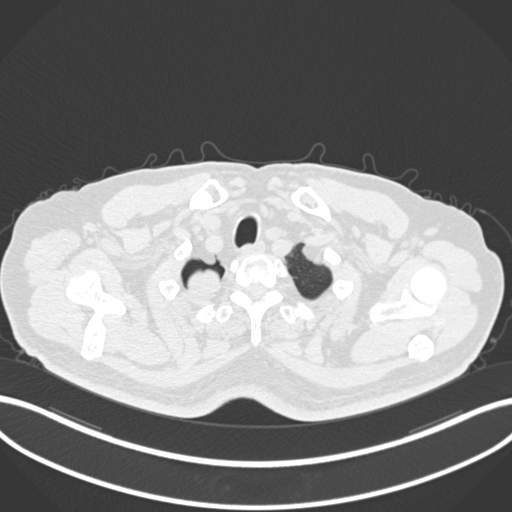
Chest CT, one axial slice. Position 202 of 218 along the scan axis. Lung window (W 1500 / L -600 HU). 512 × 512 image matrix, field of view 400 × 400 mm. Male patient, age 68 years. Case-level facts recorded for this patient, not image findings: clinical TNM (as recorded): T2a N0 M0.
Structures marked on this image (rectangle marked by the reading radiologist):
- lung tumour (recorded histology: adenocarcinoma): bounding box (x1, y1, x2, y2) in pixels: (177, 263, 226, 303)